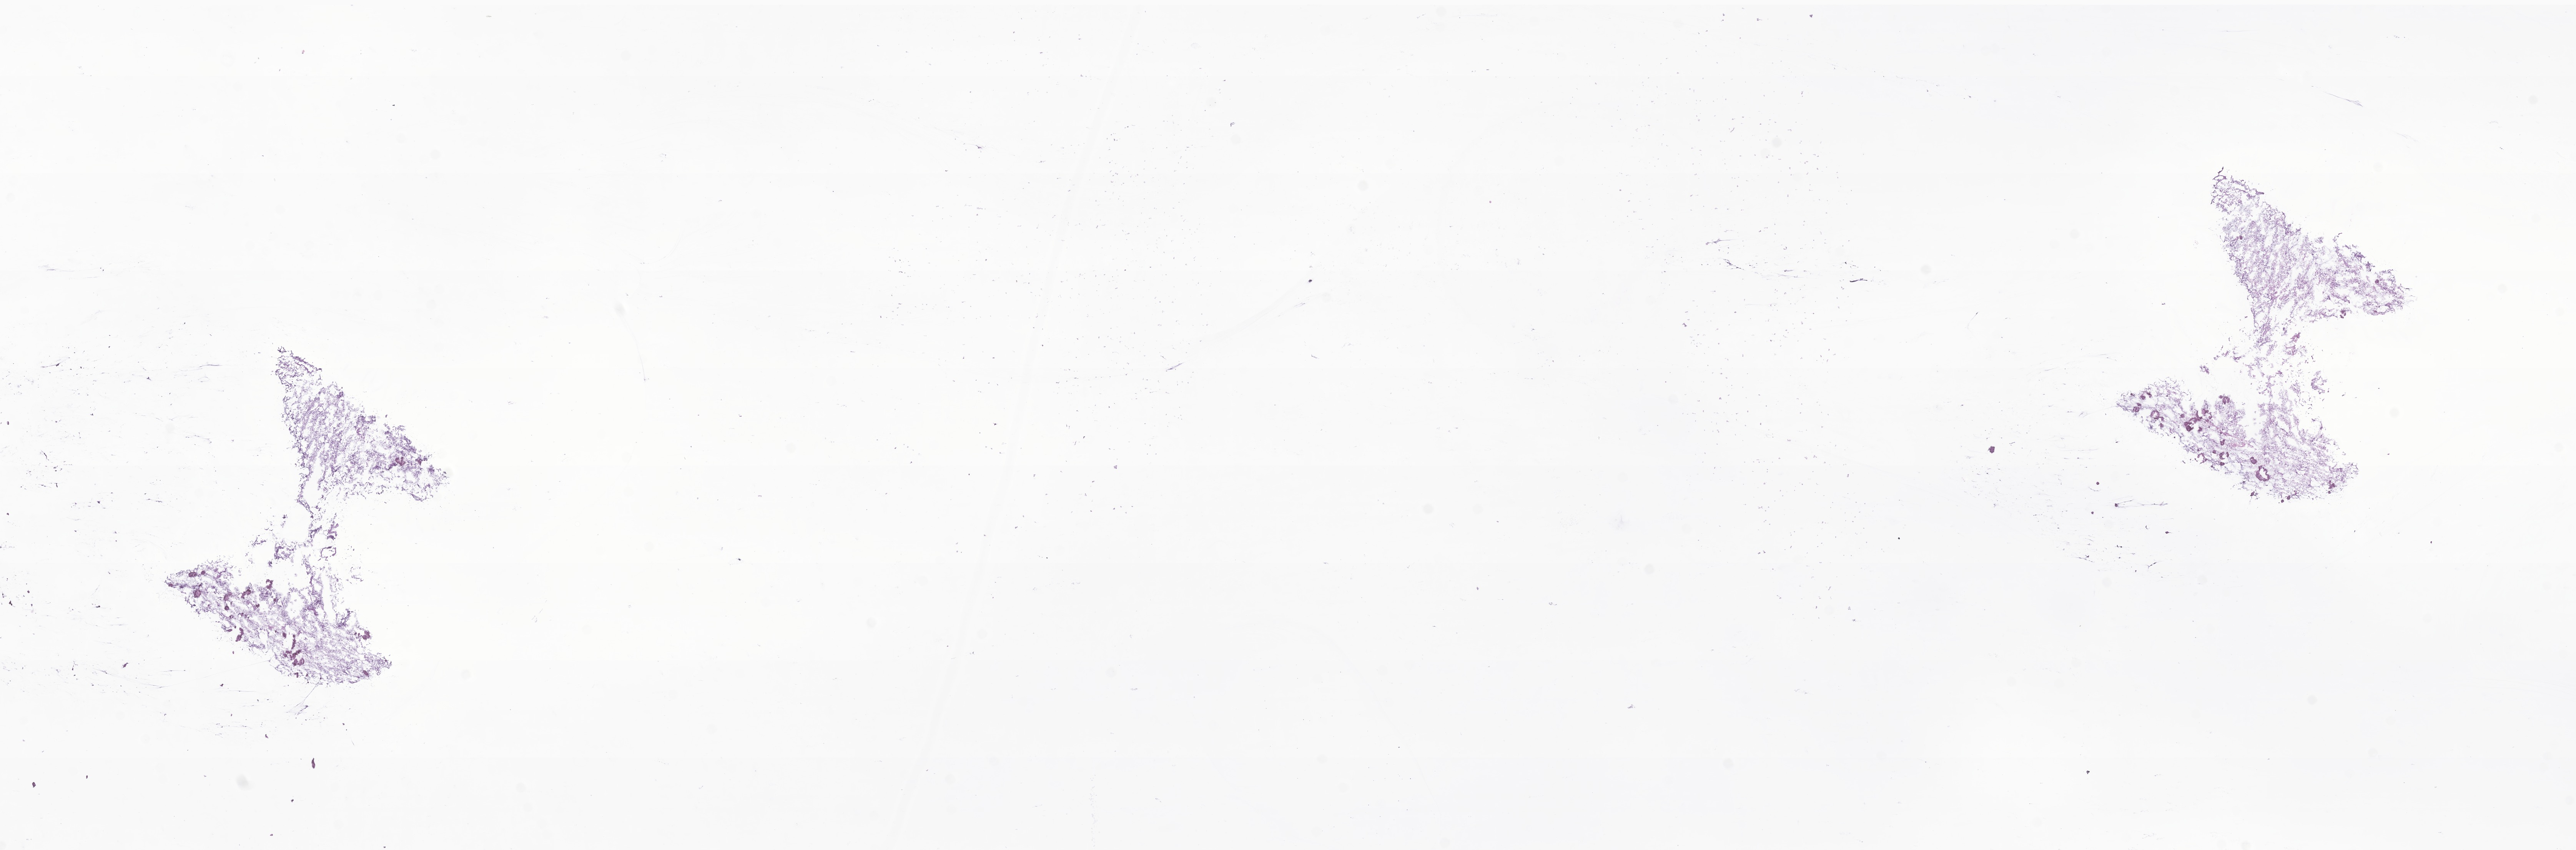
H&E whole-slide image of tumor tissue from the cerebellum — shown as a low-resolution overview of the whole scanned area (about 28.3 x 9.3 mm). Frozen section (OCT-embedded). Female patient, age 133 months.
Recorded diagnosis: Astrocytoma, NOS.